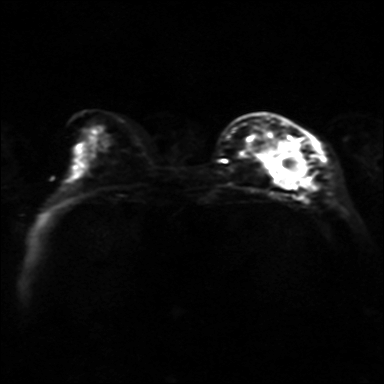
Breast MRI, one axial slice. Slice 11 of 36 in the series (ordered by position). Diffusion-weighted series; image 2 of 4 stored at this slice position (different b-values; order by instance number). 3 T. 4 mm slice thickness. 384 × 384 image matrix, field of view 320 × 320 mm. Female patient.
Outlined on this slice (outlined manually by an expert reader):
- tumour on diffusion-weighted imaging: bounding box [x1, y1, x2, y2] px = [273, 142, 306, 187]